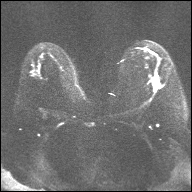
Breast MRI, one axial slice; position 20 of 32 along the scan axis; diffusion-weighted series; image 2 of 4 stored at this slice position (different b-values; order by instance number); 1.5 T; 4 mm slice thickness; 192 × 192 image matrix. Female patient.
Annotated regions visible in this slice (manually delineated by an expert):
- tumour on diffusion-weighted imaging: bounding box [x1, y1, x2, y2] px = [152, 76, 158, 83]